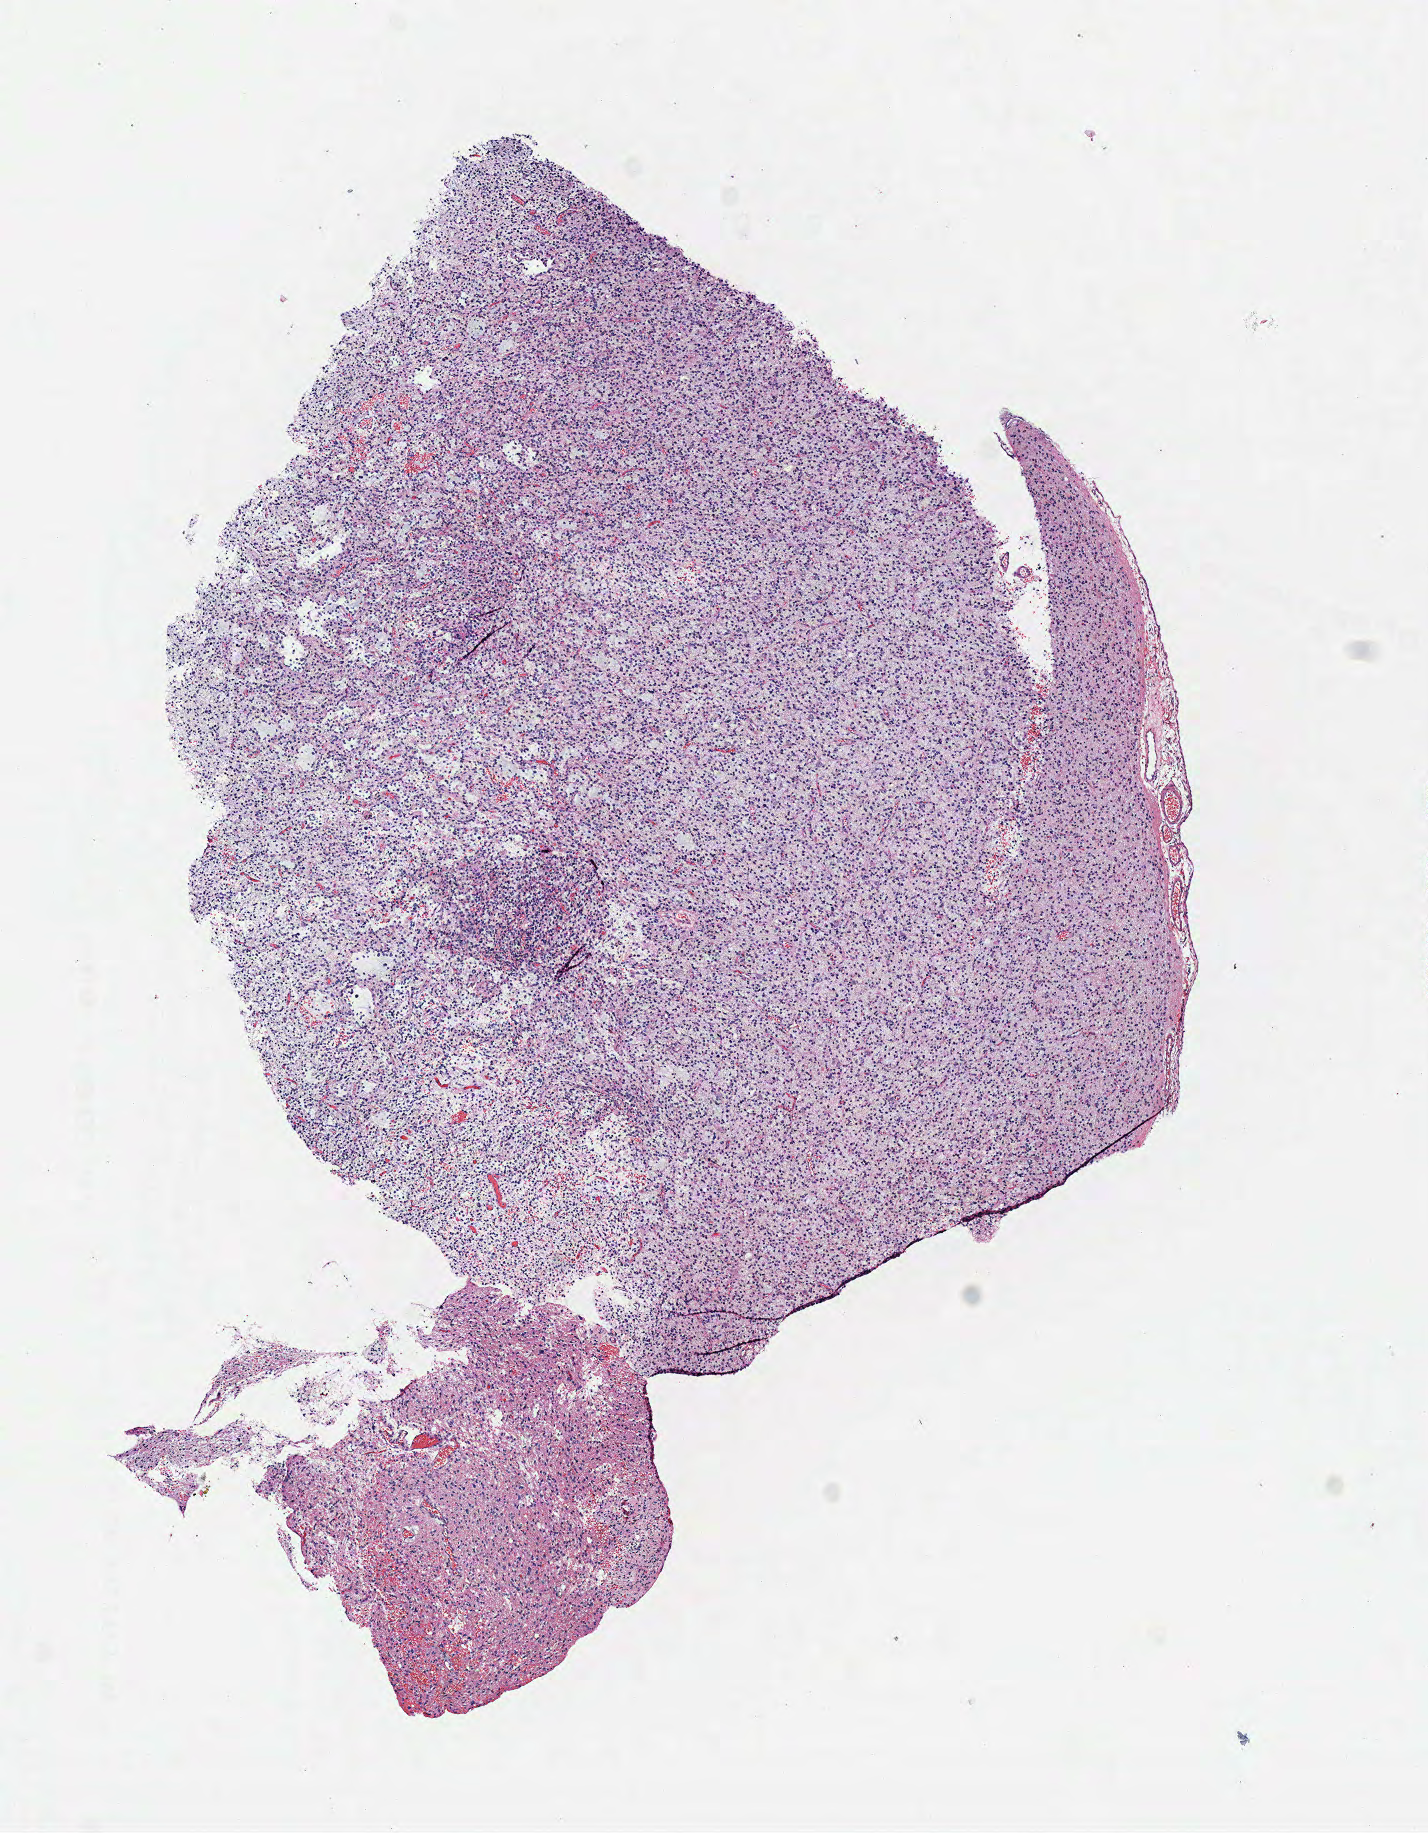
H&E whole-slide image — low-resolution overview of the scanned area, about 5.6 x 7.2 mm. Frozen section from the top of the tissue portion. Primary tumour sample from the brain. Female, age 37 years at initial diagnosis. Histologic grade: G2 (moderately differentiated). Pathologist review of this section (percent, as recorded): tumour cells 100%, tumour nuclei 75%, normal cells 0%, stromal cells 0%, necrosis 0%.
Laterality: left. Pathologic diagnosis: Mixed glioma.